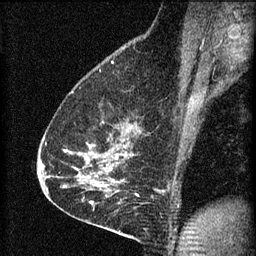
Breast MRI (dynamic contrast-enhanced), one sagittal slice. Position 42 of 60 along the scan axis. 3 images stored at this slice position (order not interpretable as contrast timing). 1.5 T. TE 4.2 ms, TR 8.2 ms. 2 mm slice thickness. 256 × 256 image matrix, field of view 180 × 180 mm. Patient: female, 59 years.
Outlined on this slice (semi-automatic segmentation, software-assisted and operator-edited):
- analysis volume of interest (the breast-tissue region the enhancement analysis was run in; not a lesion): bounding box <61,108,134,161> (left, top, right, bottom; pixels)
- tumour enhancement mask (voxels above the 70 % enhancement threshold inside the analysis volume of interest): <91,146,126,159>